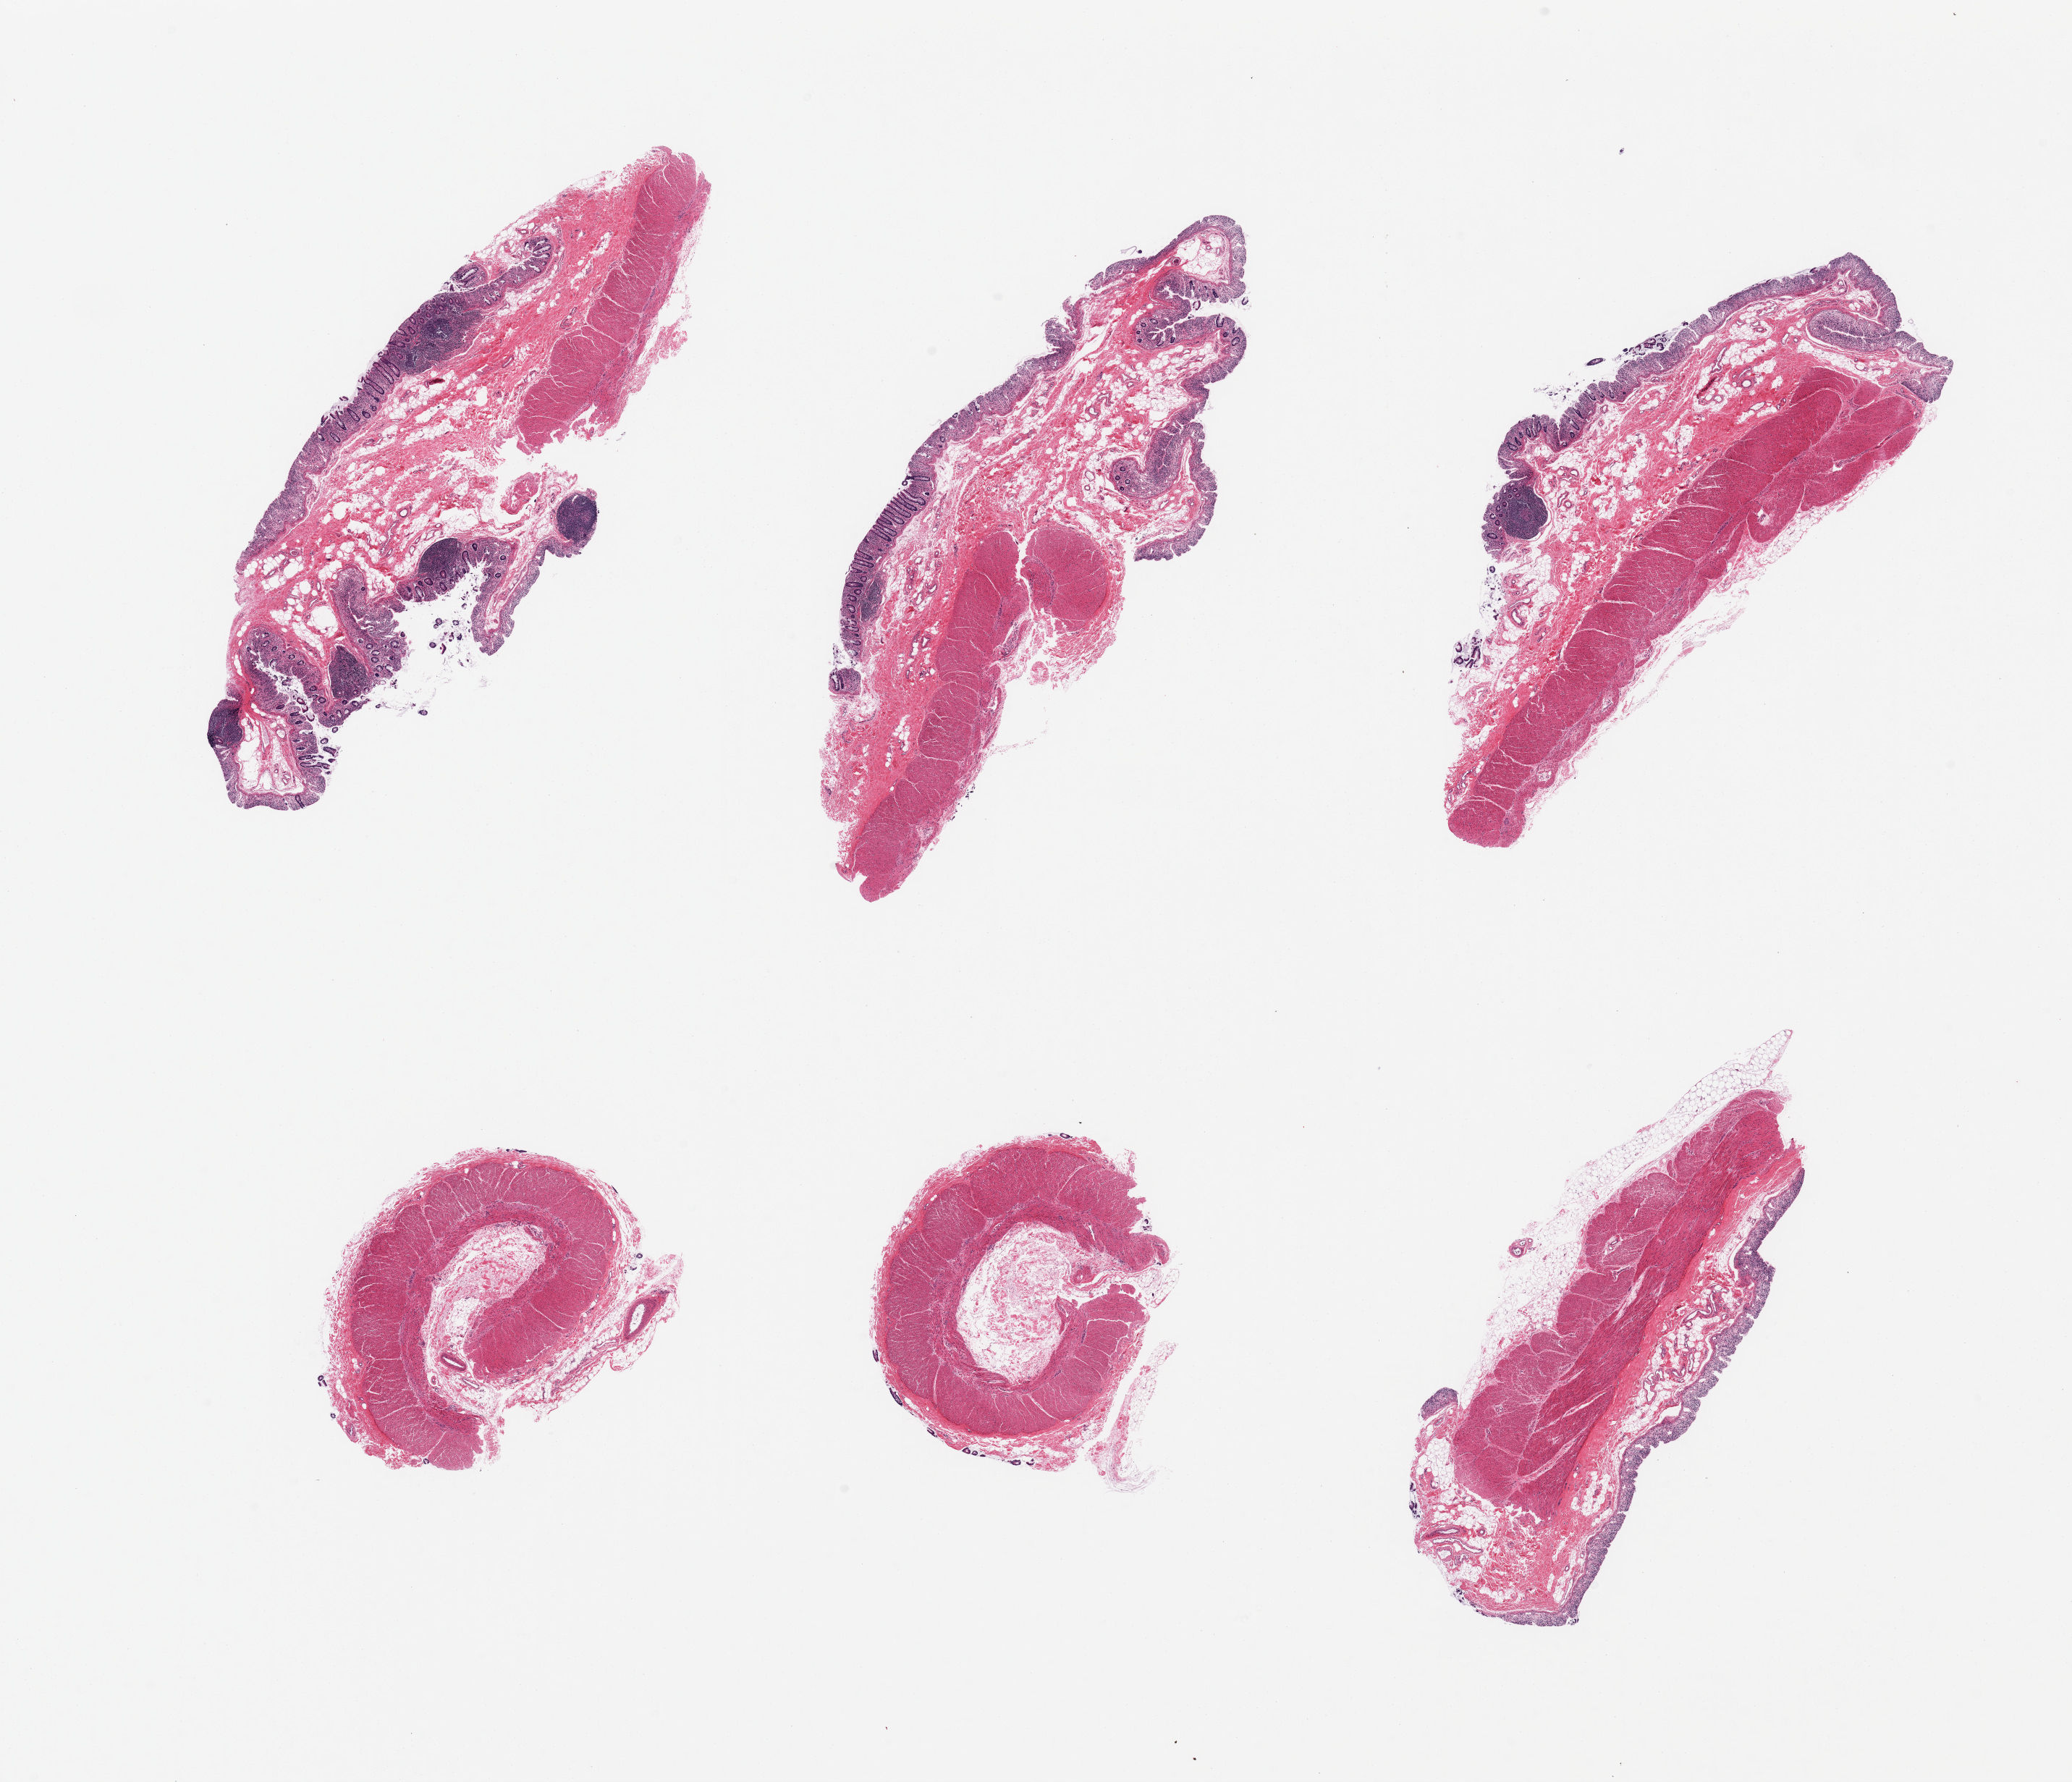
Whole-slide image, hematoxylin and eosin (H&E) stain — whole scanned area (about 22.6 x 19.5 mm, from a 20x scan) shown as a low-resolution overview; PAXgene-fixed paraffin-embedded (PFPE) section; section of ileum (target tissue); tissue donor sample. Donor sex: female.
Reviewer comment on this tissue sample: 6 pieces; moderately autolyzed mucosa; 3 pieces with target lymphoid aggregates representing ~ 15% tissue and non-target muscularis present.